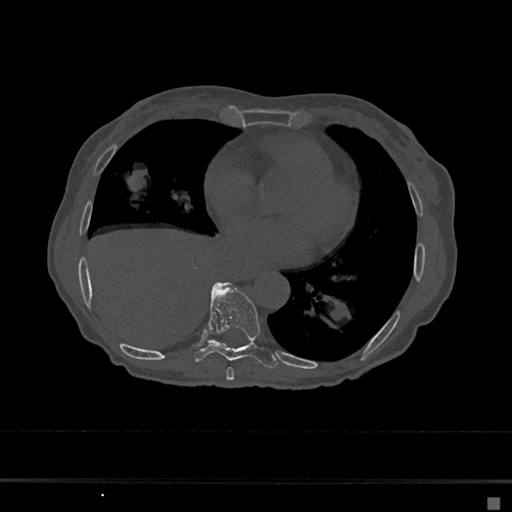
CT including the spine, one axial slice. Slice 322 of 797 in the series (ordered by position). Bone window (W 1800 / L 400 HU). 512 × 512 image matrix. Patient: female, 68 years. Case-level facts recorded for this patient, not image findings: primary cancer: renal.
Annotated regions visible in this slice (semi-automatic segmentation, software-assisted and operator-edited):
- T7 vertebra: bounding box (x1, y1, x2, y2) in pixels: (226, 367, 235, 381)
- T8 vertebra: (195, 282, 278, 368)
- T9 vertebra: (216, 282, 224, 287)